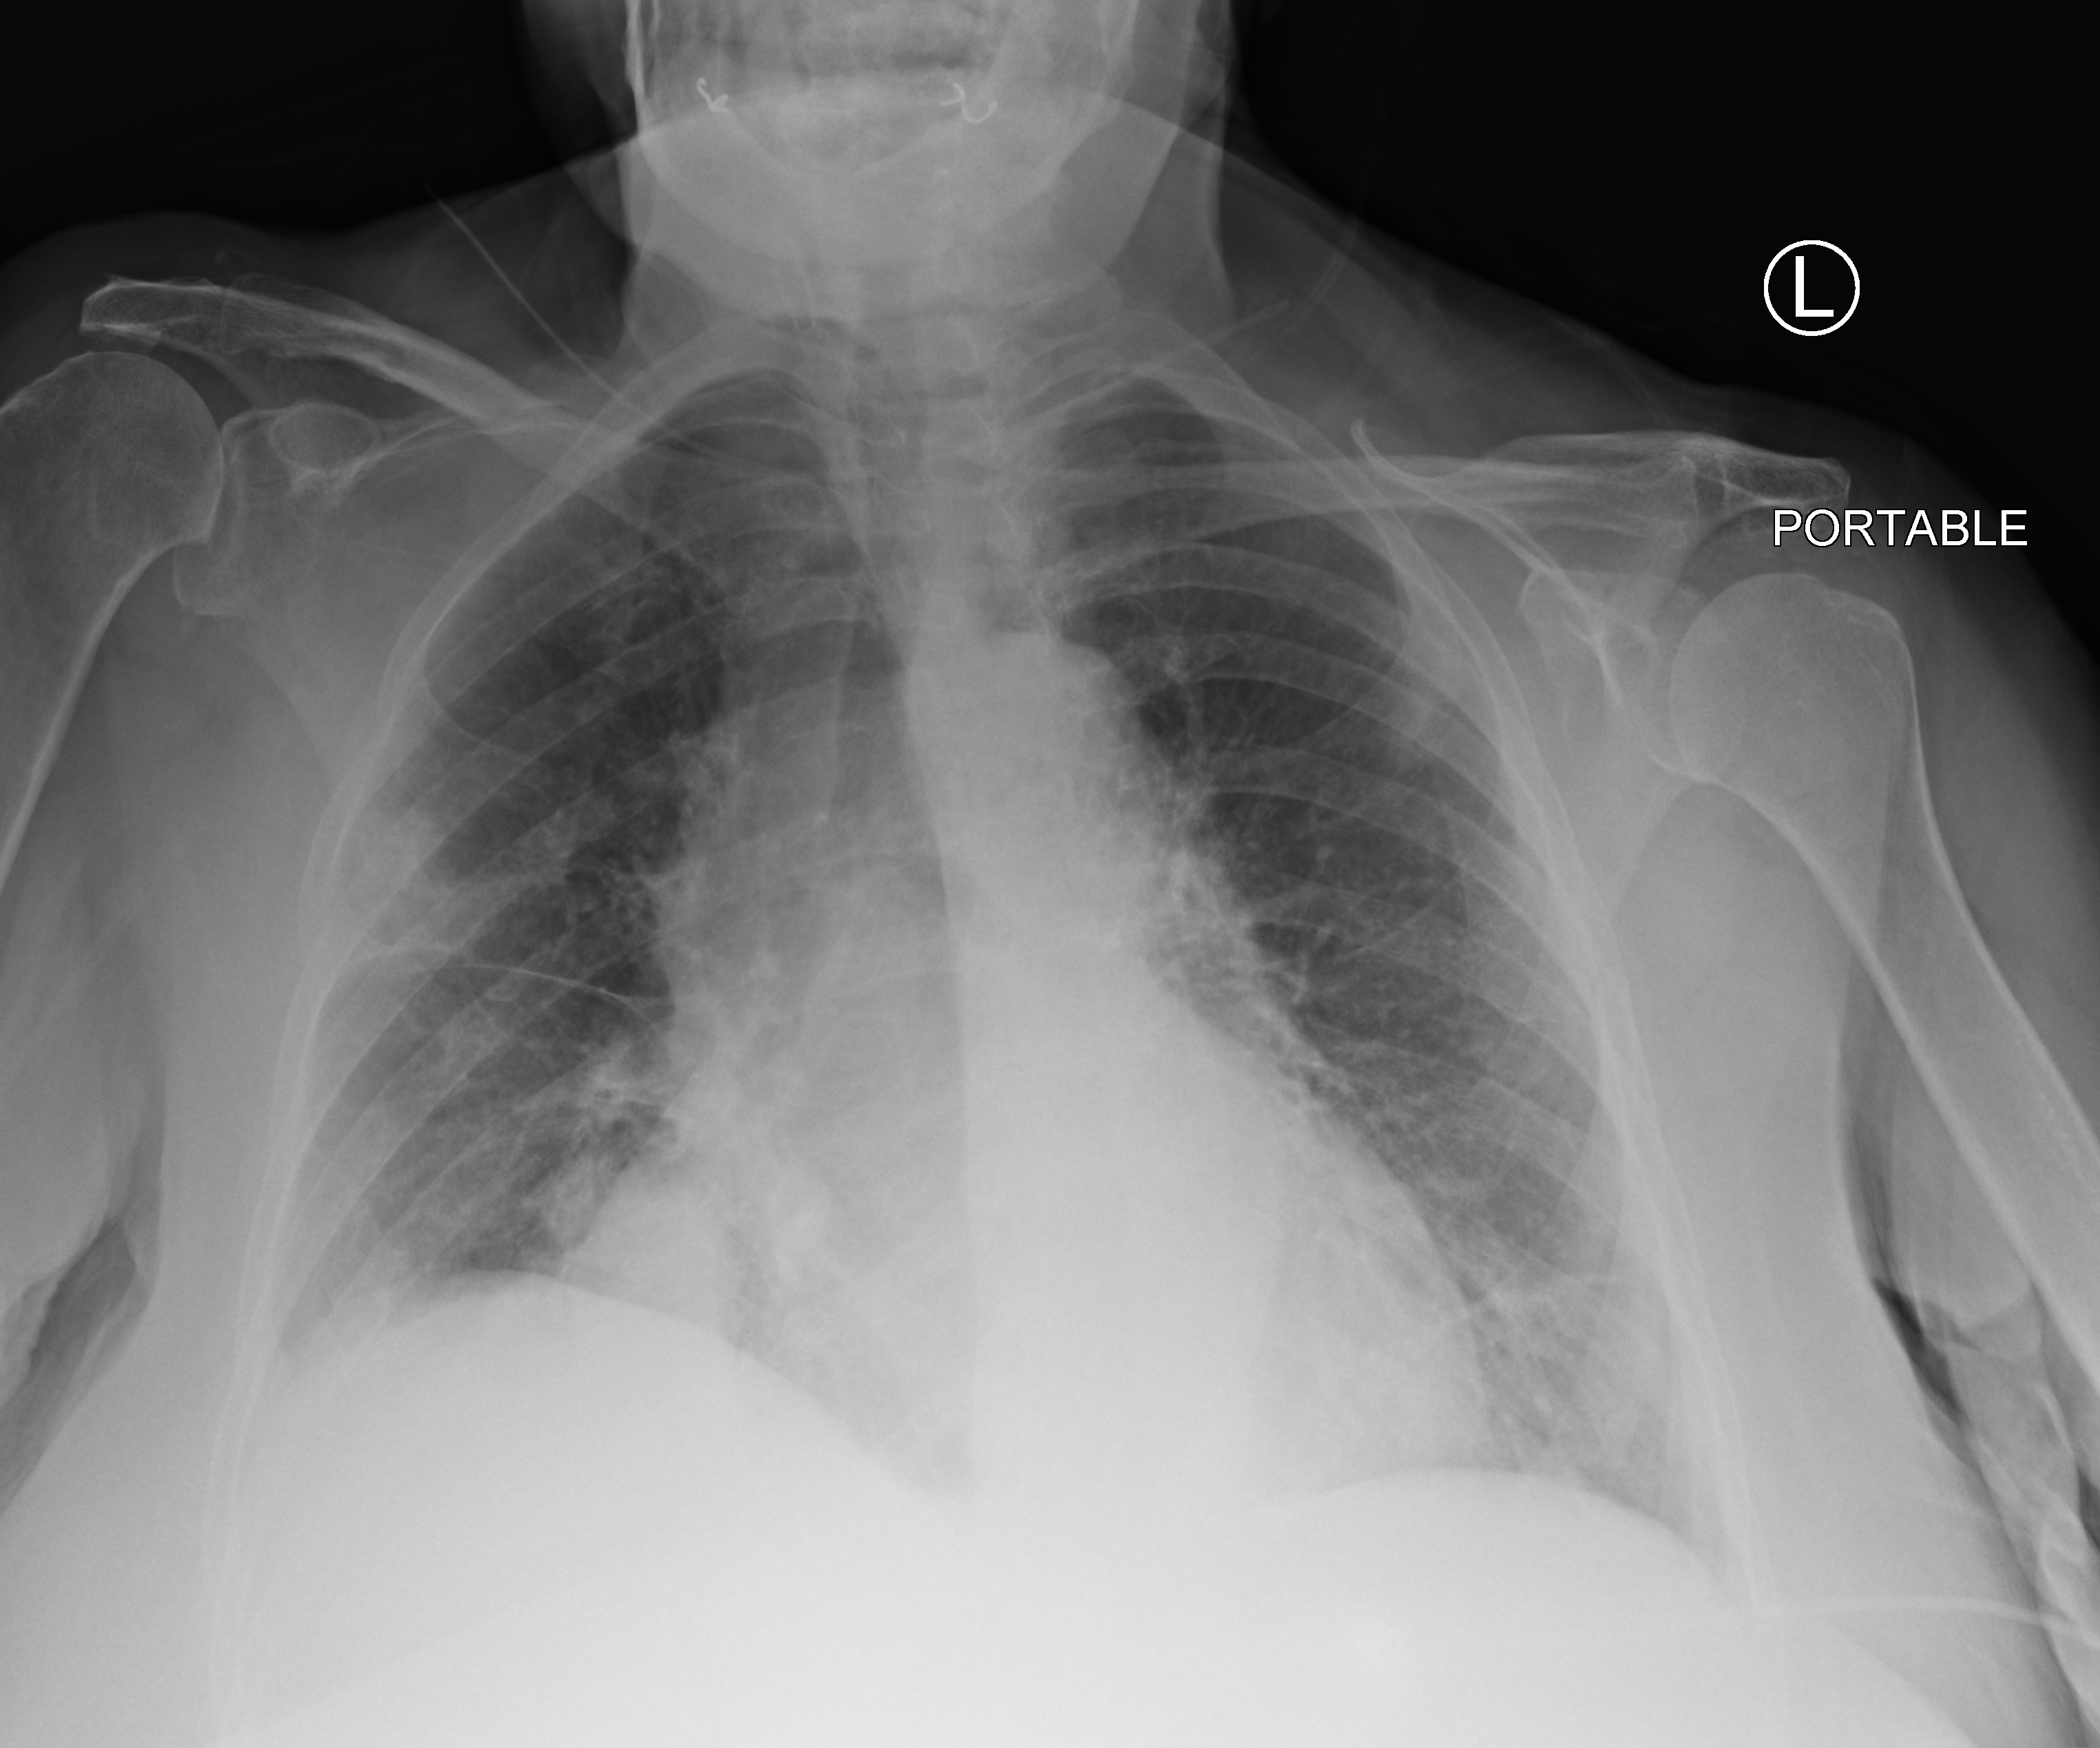
Bedside chest radiograph (computed radiography), anteroposterior (AP) projection. Female patient hospitalised with COVID-19, age 75–90 years.
From the hospital-stay record, not from the radiograph (when in the stay this image was taken is not recorded):
- mechanically ventilated during this hospital stay: no
- admitted to intensive care during this hospital stay: no
- length of hospital stay: 5 days